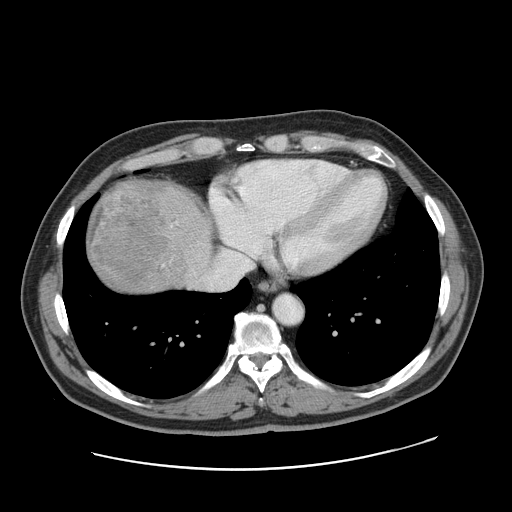
Contrast-enhanced abdominal CT, one axial slice. Slice 151 of 178 in the series (ordered by position). 120 kVp. Intravenous contrast given. Soft-tissue window (W 400 / L 40 HU). 512 × 512 image matrix, field of view 403 × 403 mm. Male patient, age 63 years. Case-level facts recorded for this patient, not image findings: diagnosis: colorectal cancer liver metastases, imaged before liver resection; multiple liver metastases: yes; largest metastasis: 8 cm.
Annotated regions visible in this slice (manually delineated by an expert):
- liver: bounding box [x1, y1, x2, y2] px = [85, 180, 214, 295]
- planned liver remnant (the part of the liver to remain after resection): [187, 196, 213, 239]
- liver metastasis: [89, 184, 165, 281]